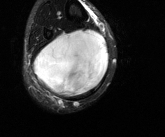
MRI of an extremity soft-tissue mass, one axial slice. Slice 48 of 81 in the series (ordered by position). T2-weighted fat-saturated. MR volume resampled by the dataset authors to the PET/CT grid (not the native acquisition matrix). 3.27 mm slice thickness. 165 × 137 image matrix. Male patient. Case-level facts recorded for this patient, not image findings: histological type: liposarcoma - round cell; grade: high; site of the primary tumour: right calf.
Annotated regions visible in this slice (expert contour drawn on MRI and transferred to this co-registered scan by the dataset authors):
- gross tumour volume (mass): bounding box (x1, y1, x2, y2) in pixels: (34, 29, 109, 97)